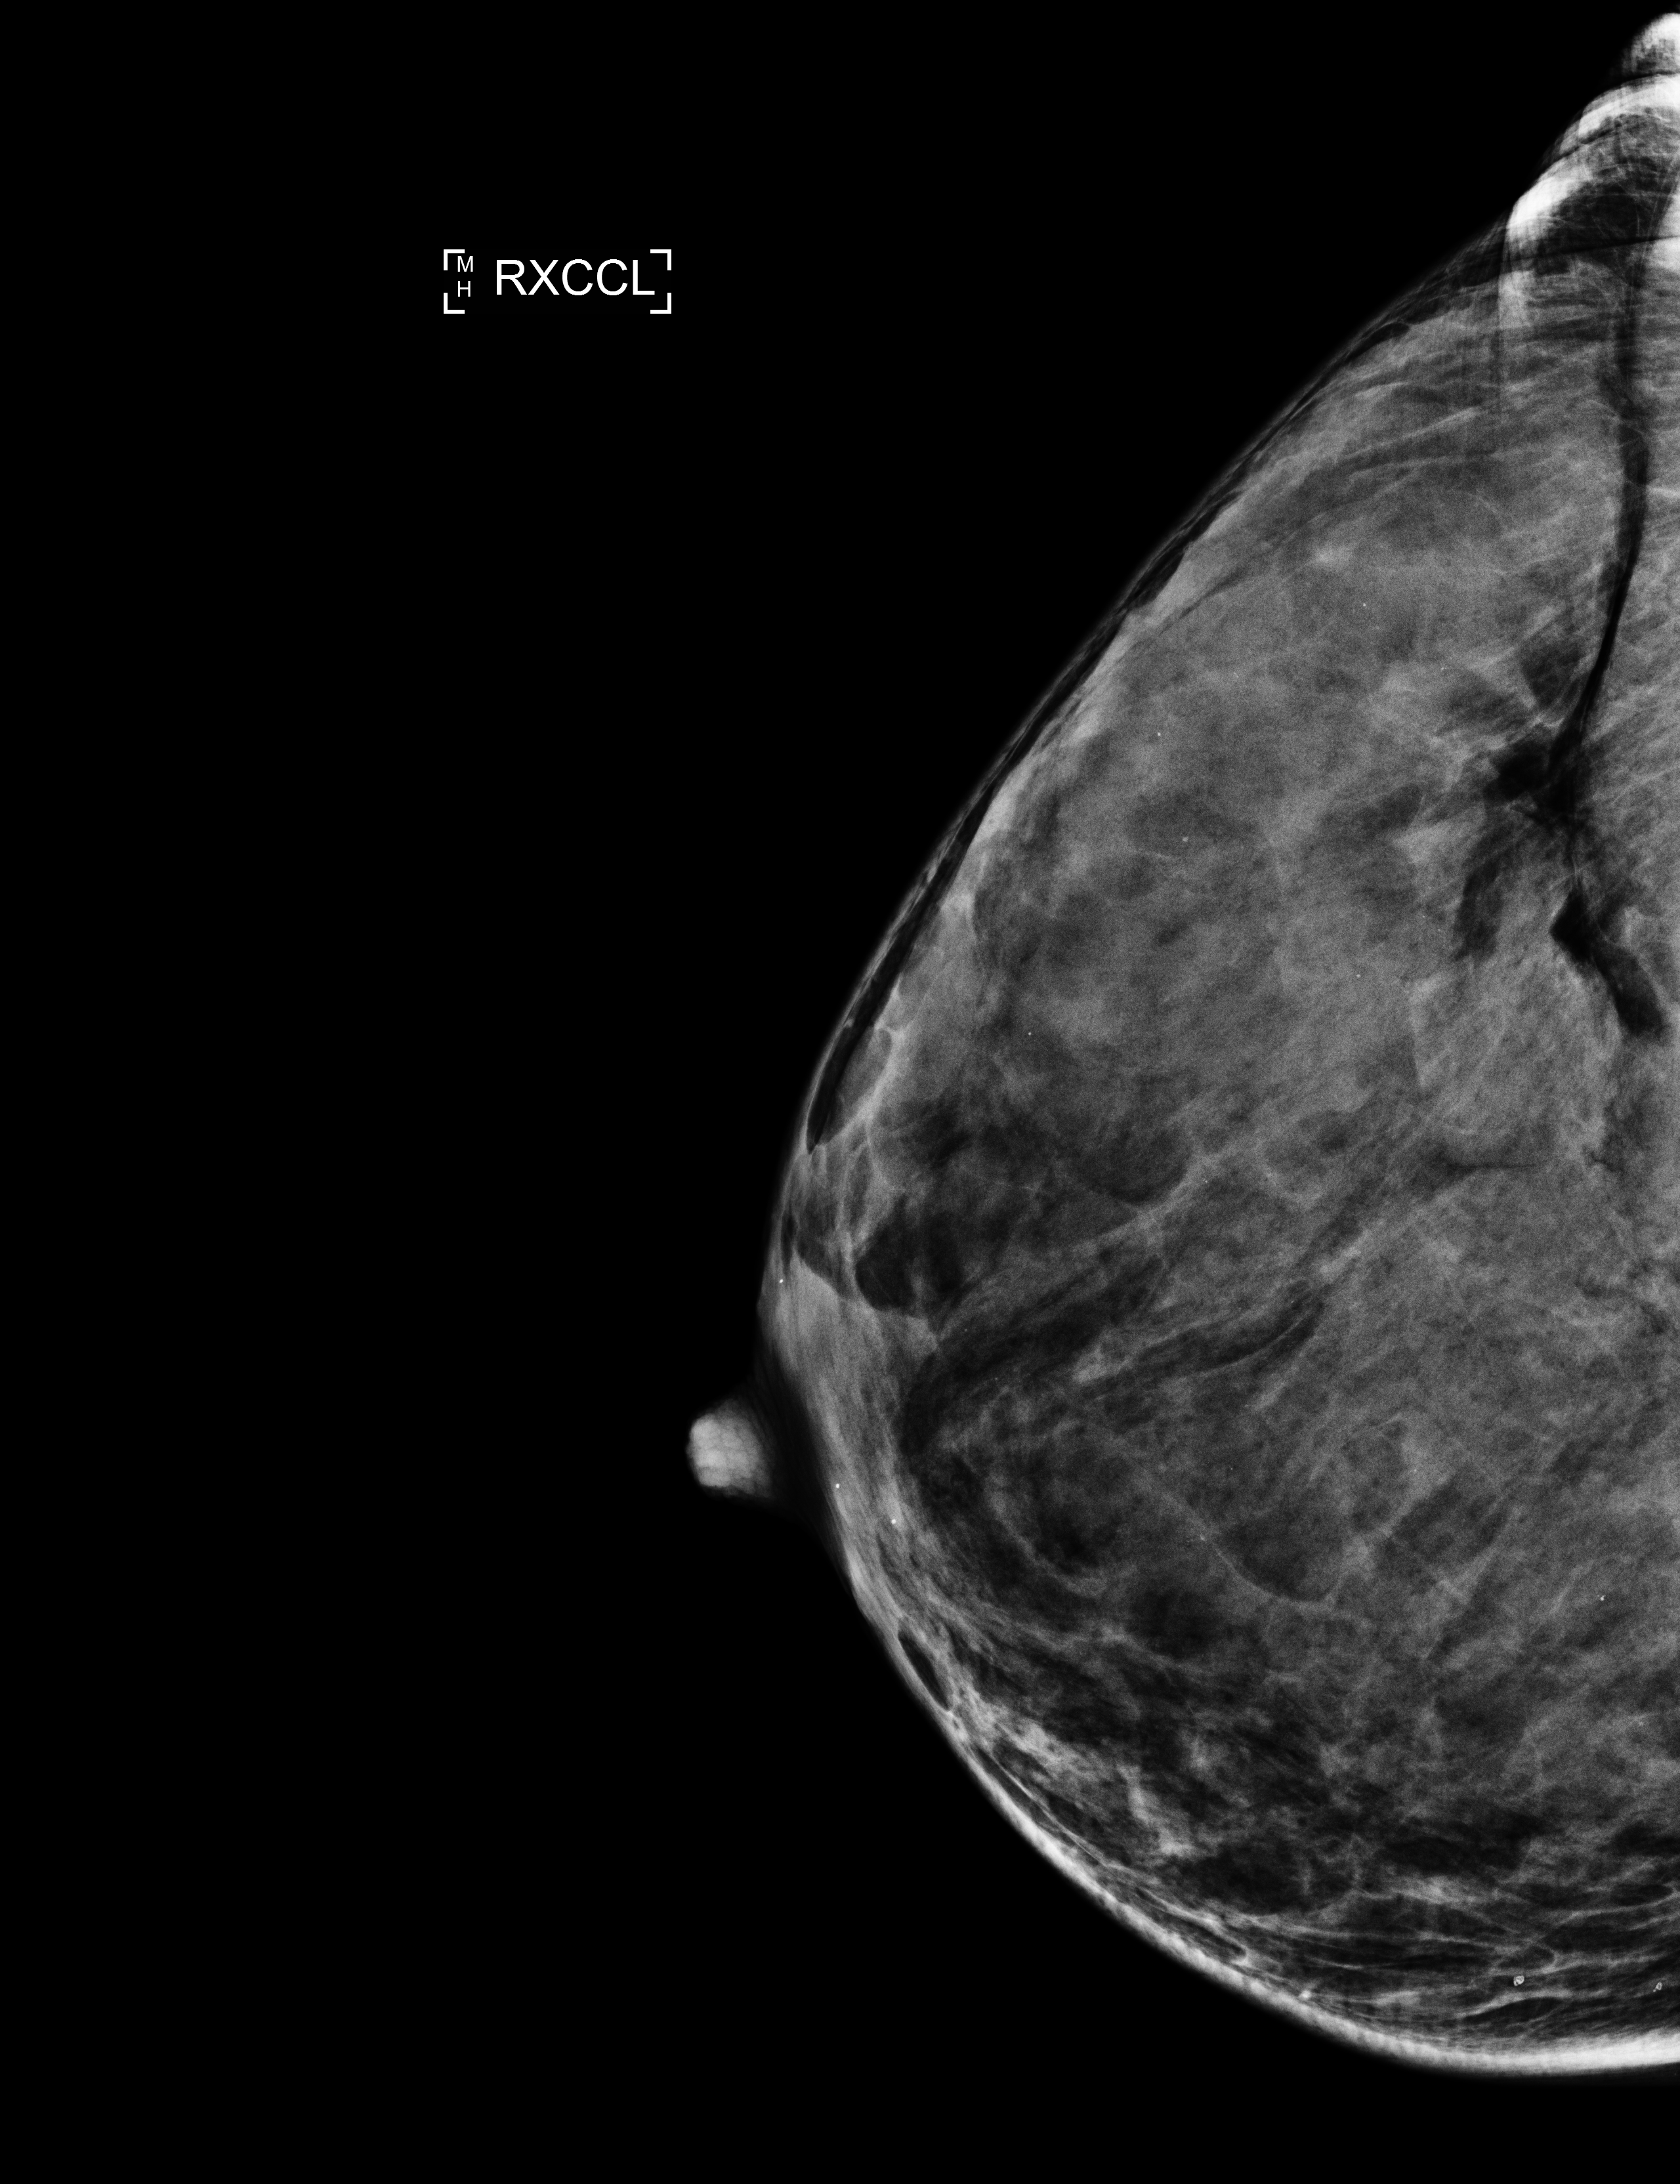
Annual screening mammography examination. Patient: female, 42 years.
Image type: full-field digital mammogram. Breast: right. Projection: laterally exaggerated craniocaudal (XCCL) view.